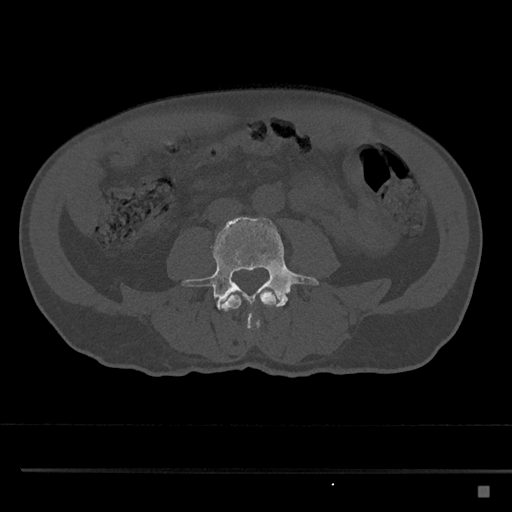
CT including the spine, one axial slice; position 652 of 797 along the scan axis; reconstruction kernel Br40s/3; 120 kVp; bone window (W 1800 / L 400 HU); 0.5 mm slice thickness; 512 × 512 image matrix, field of view 391 × 391 mm. Male patient, age 59 years. Case-level facts recorded for this patient, not image findings: primary cancer: prostate.
Structures marked on this image (semi-automatically segmented with operator editing):
- L3 vertebra: bounding box [x1, y1, x2, y2] px = [221, 289, 277, 330]
- L4 vertebra: [181, 217, 319, 332]